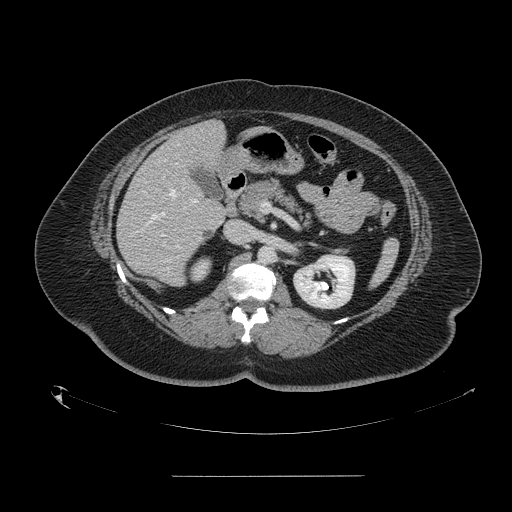
Contrast-enhanced abdominal CT, one axial slice; position 77 of 164 along the scan axis; intravenous contrast given; soft-tissue window (W 400 / L 40 HU); 2.5 mm slice thickness; 512 × 512 image matrix, field of view 495 × 495 mm. Female patient, age 52 years. Case-level facts recorded for this patient, not image findings: diagnosis: colorectal cancer liver metastases, imaged before liver resection; multiple liver metastases: yes; largest metastasis: 3.5 cm; disease in both lobes: no.
Outlined on this slice (expert manual segmentation):
- hepatic veins: bounding box <143,163,186,228> (left, top, right, bottom; pixels)
- liver: <118,122,226,286>
- planned liver remnant (the part of the liver to remain after resection): <177,122,225,168>
- portal vein (with intrahepatic branches): <161,177,196,237>
- liver metastasis: <203,228,212,237>